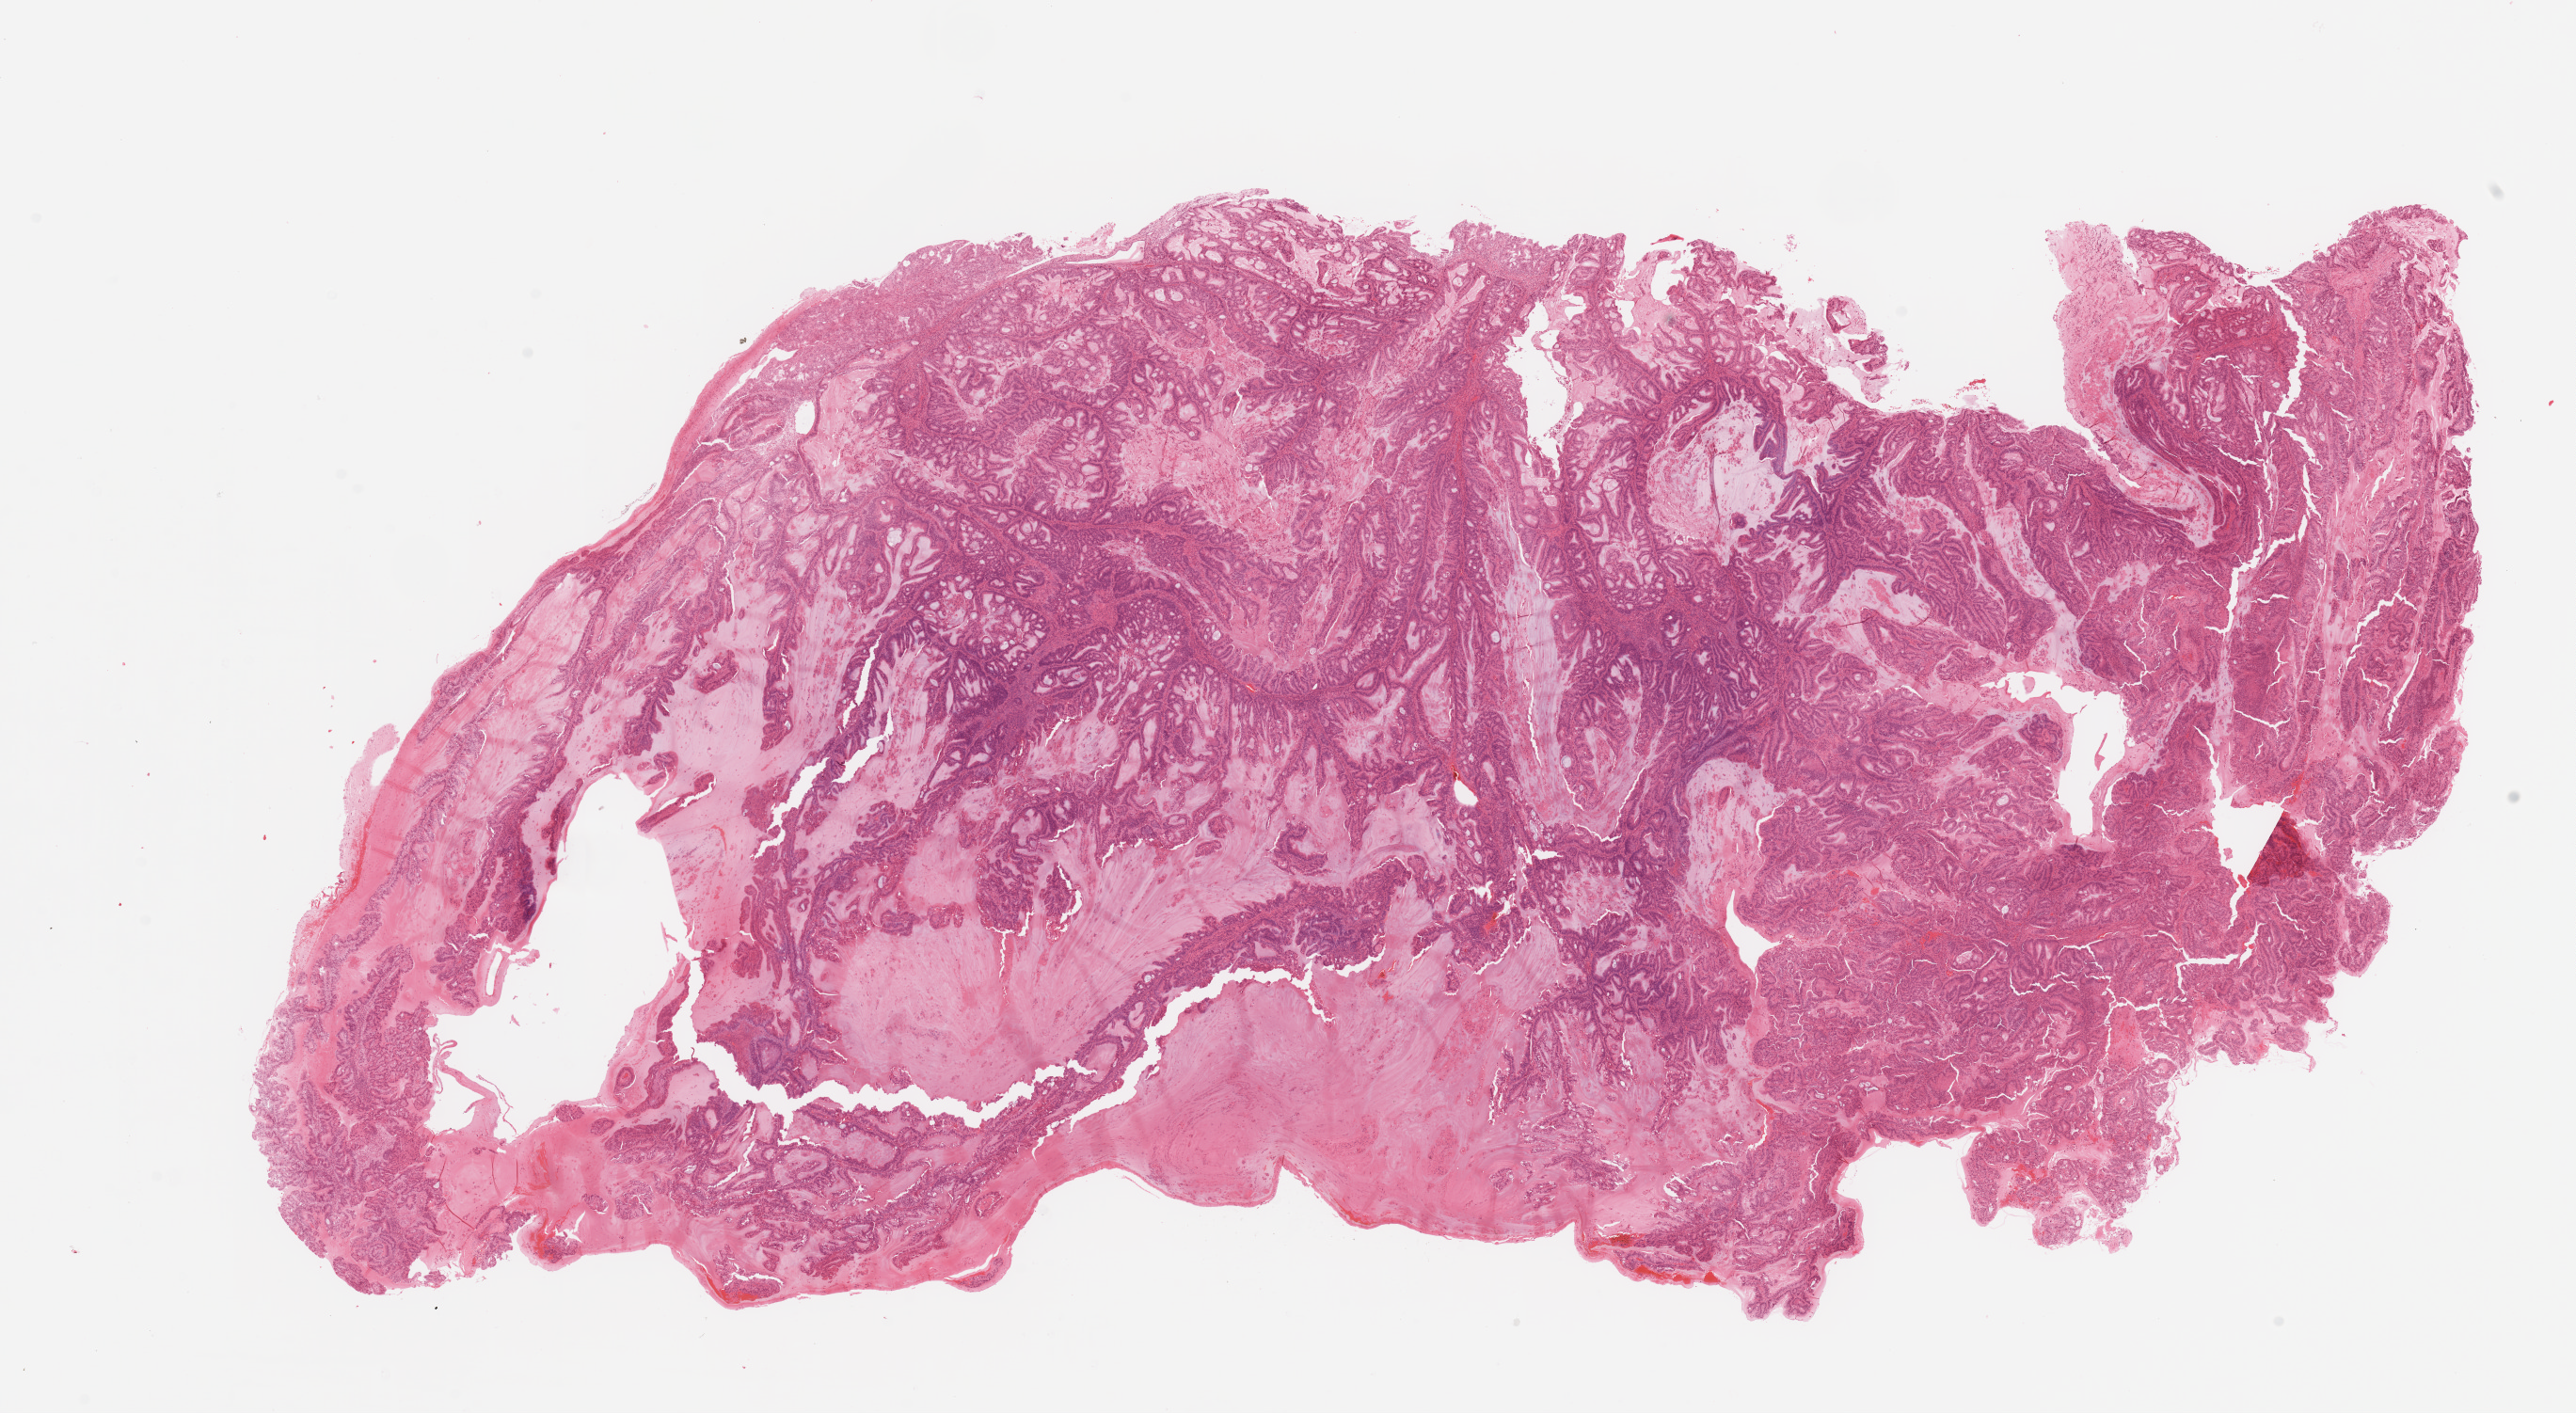
H&E whole-slide image, low-resolution overview of the scanned area, about 21.7 x 11.9 mm; tumour tissue sample, uterus. 77-year-old female patient. Histologic grade: G1 (well differentiated).
Histologic diagnosis: Endometrioid adenocarcinoma, NOS.